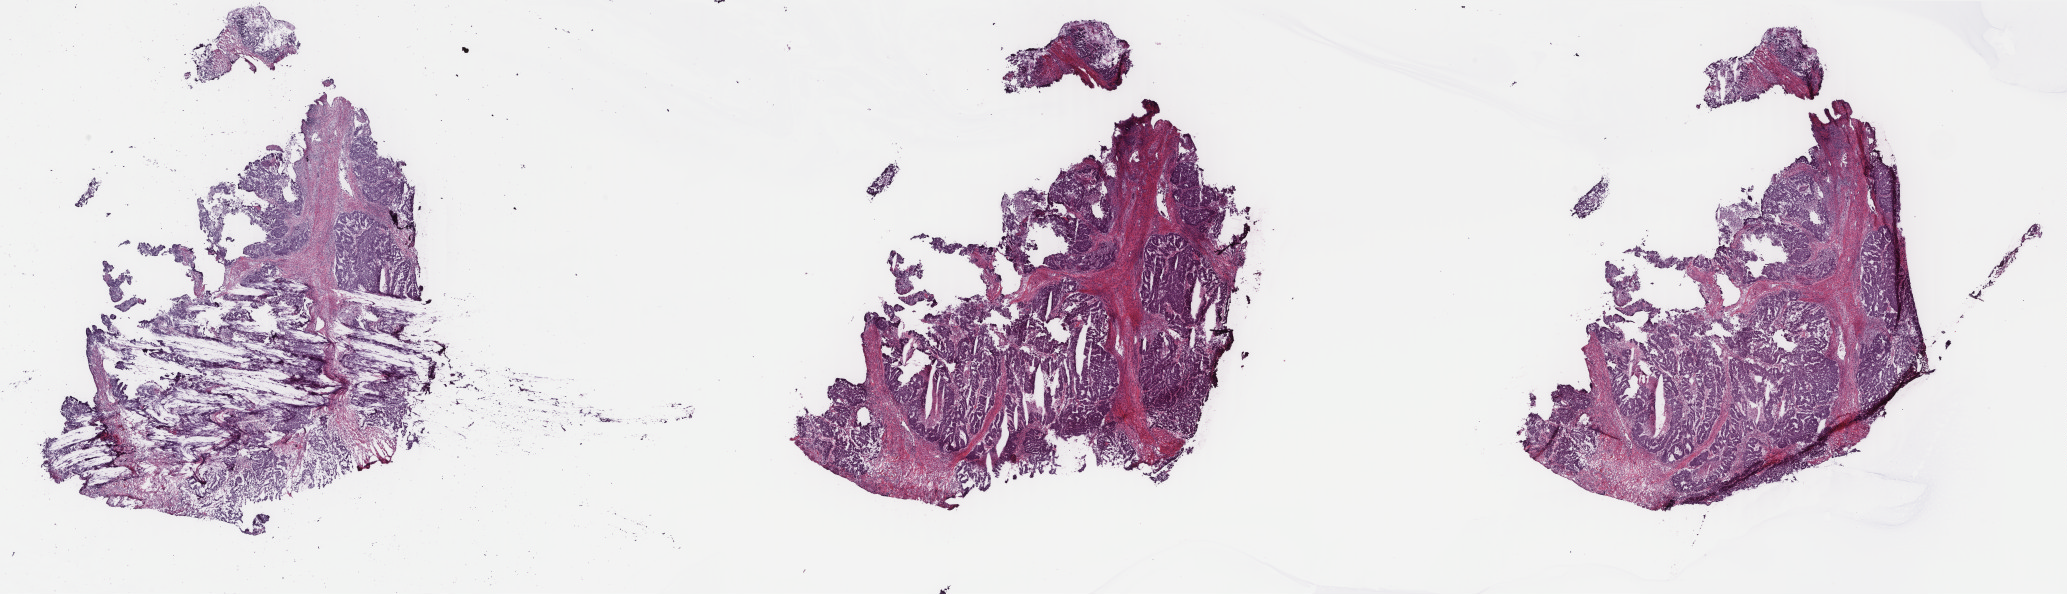
Digitized Hematoxylin and eosin (H&E) stained tissue section (whole slide), whole scanned area (about 32.8 x 9.4 mm, from a 40x scan) shown as a low-resolution overview. Frozen section. Sample: primary tumour, uterus. Female, age 64 years at initial diagnosis. Histologic grade: G3 (poorly differentiated). Composition of this section per pathologist review: tumour cells 90%, tumour nuclei 75%, normal cells 0%, stromal cells 0%, necrosis 10%. Inflammatory infiltration, as recorded: lymphocyte infiltration 5%, monocyte infiltration 1%, neutrophil infiltration 0%.
* FIGO stage: IVB
* pathologic diagnosis: Serous cystadenocarcinoma, NOS (endometrium)